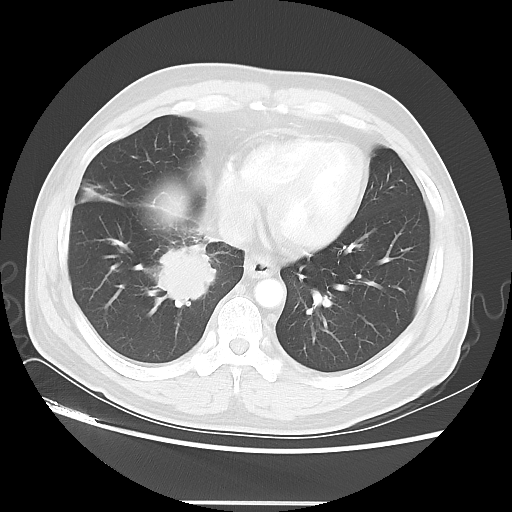
Chest CT, one axial slice; position 14 of 48 along the scan axis; reconstruction kernel LUNG; 120 kVp; lung window (W 1500 / L -600 HU); 5 mm slice thickness; 512 × 512 image matrix, field of view 390 × 390 mm. Male patient, age 53 years. Case-level facts recorded for this patient, not image findings: clinical TNM (as recorded): T2 N3 M0.
Outlined on this slice (rectangle marked by the reading radiologist):
- lung tumour (recorded histology: small cell carcinoma): bounding box <154,235,226,314> (left, top, right, bottom; pixels)